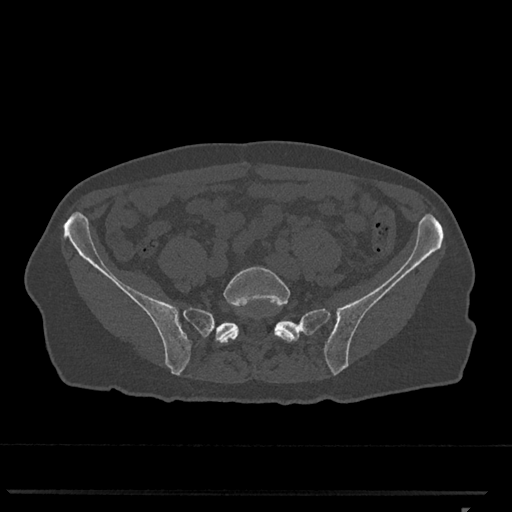
CT including the spine, one axial slice; position 127 of 793 along the scan axis; bone window (W 1800 / L 400 HU); 0.5 mm slice thickness; 512 × 512 image matrix, field of view 380 × 380 mm. Female patient, age 62 years. Case-level facts recorded for this patient, not image findings: primary cancer: renal.
Outlined on this slice (semi-automatically segmented with operator editing):
- L5 vertebra: bounding box <217,266,297,343> (left, top, right, bottom; pixels)